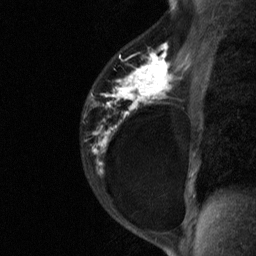
Breast MRI (dynamic contrast-enhanced), one sagittal slice; slice 45 of 64 in the series (ordered by position); dynamic contrast-enhanced study with each time point stored as its own series, time point 2 of 3 at this slice position (early post-contrast, ordered by acquisition time); 1.5 T; TE 4.8 ms, TR 27 ms; 256 × 256 image matrix, field of view 180 × 180 mm. Female patient, age 34 years. Case-level facts recorded for this patient, not image findings: setting: breast cancer imaged before/during neoadjuvant chemotherapy; receptor status: HR-positive, HER2-negative.
Structures marked on this image (semi-automatic segmentation, software-assisted and operator-edited):
- analysis volume of interest (the breast-tissue region the enhancement analysis was run in; not a lesion): bounding box <81,44,181,191> (left, top, right, bottom; pixels)
- tumour enhancement mask (voxels above the 90 % enhancement threshold inside the analysis volume of interest): <93,44,173,171>